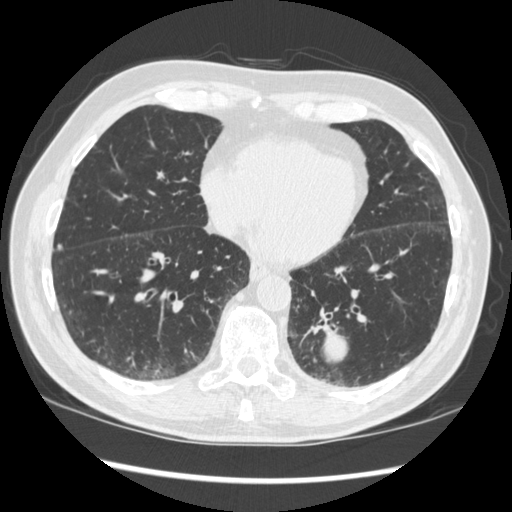
Low-dose screening chest CT, one axial slice. Slice 115 of 348 in the series (ordered by position). 120 kVp. Lung window (W 1500 / L -600 HU). 1.25 mm slice thickness. 512 × 512 image matrix, field of view 360 × 360 mm.
Annotated regions visible in this slice (expert manual segmentation):
- lesion 1 (tumor, lower lobe of left lung): bounding box (x1, y1, x2, y2) in pixels: (323, 326, 347, 363)